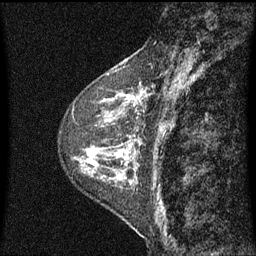
Breast MRI (dynamic contrast-enhanced), one sagittal slice. Slice 22 of 60 in the series (ordered by position). Dynamic contrast-enhanced series, image 2 of 3 at this slice position (ordered by acquisition). 1.5 T. TE 4.2 ms, TR 8 ms. 2 mm slice thickness. 256 × 256 image matrix, field of view 200 × 200 mm. Female patient, age 48 years.
Annotated regions visible in this slice (semi-automatic segmentation, software-assisted and operator-edited):
- analysis volume of interest (the breast-tissue region the enhancement analysis was run in; not a lesion): bounding box (x1, y1, x2, y2) in pixels: (103, 74, 145, 139)
- tumour enhancement mask (voxels above the 70 % enhancement threshold inside the analysis volume of interest): (104, 82, 145, 139)